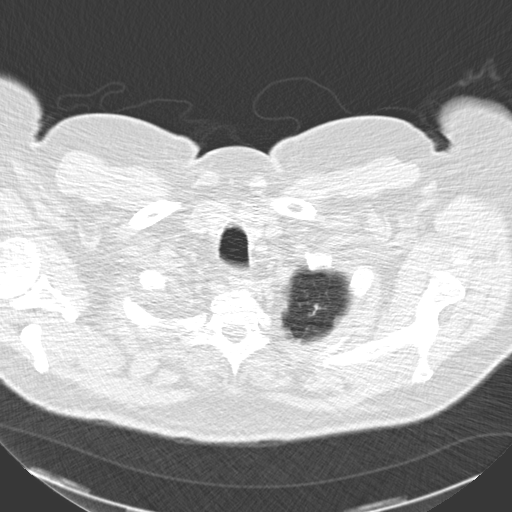
Low-dose screening chest CT, axial slice. Baseline annual screen. Lung window (W 1500 / L -600 HU). Standard (soft-tissue) reconstruction kernel (B30f). 512 × 512 image matrix, field of view 366 × 366 mm. Male participant, aged 67 years at enrolment.
- Expert-annotated lung lesion, bounding box [x1, y1, x2, y2] px = [299, 296, 332, 327].
- Screening reader's record for this exam: no non-calcified nodule ≥4 mm recorded.
- Official screen result: negative screen, minor abnormalities not suspicious for lung cancer.
- Later outcome: lung cancer diagnosed 891 days after this screen — adenocarcinoma, NOS, left upper lobe, moderately differentiated (G2), stage IIA (AJCC 6th edition), 18 mm at pathology.